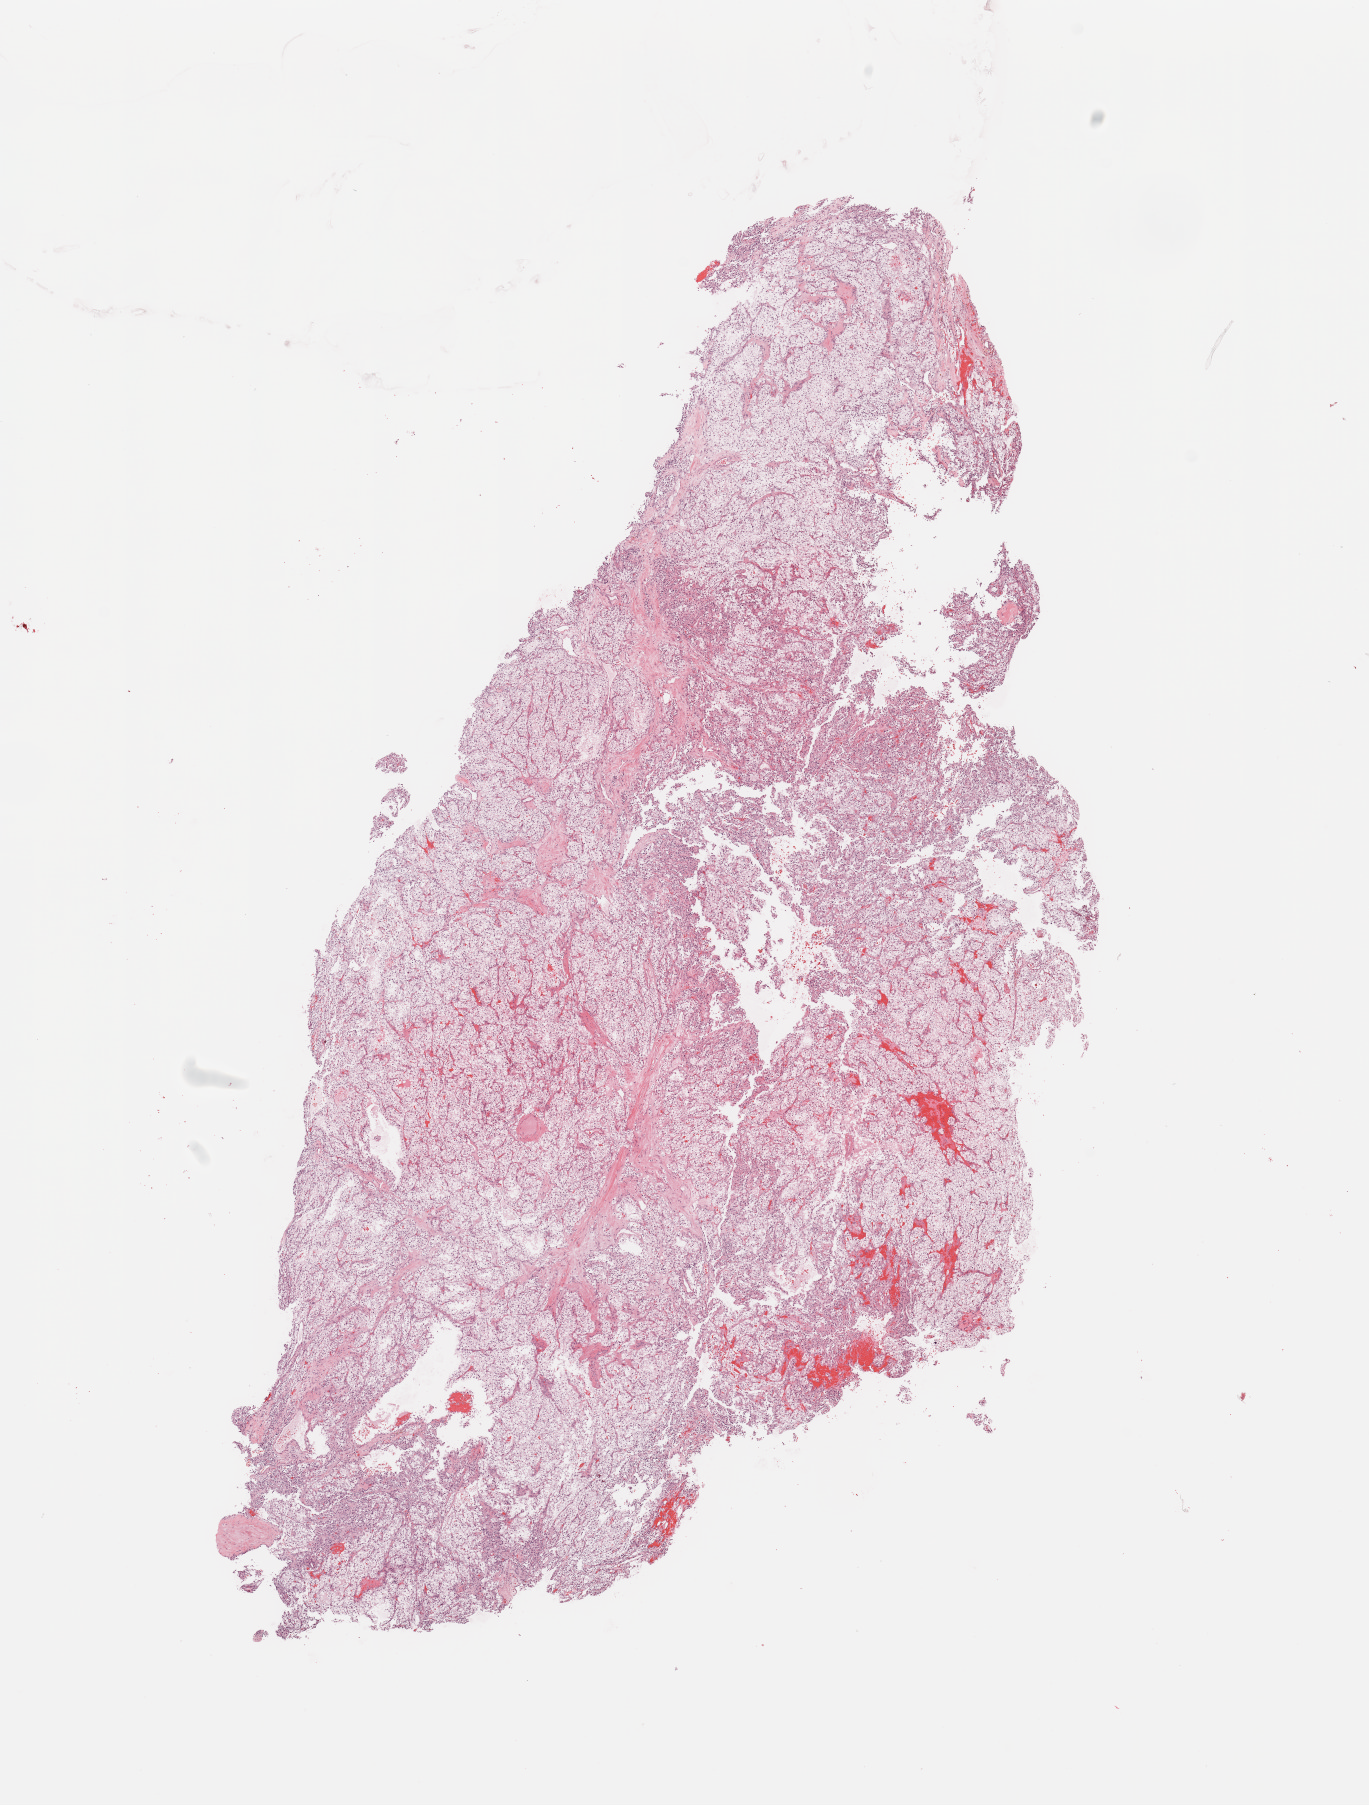
Whole-slide histology image, H&E-stained — whole scanned area (about 10.8 x 14.3 mm, acquisition: 20x scan) shown as a low-resolution overview. Tumour tissue sample, sampled site: kidney. 41-year-old male patient.
Diagnosis: Renal cell carcinoma, NOS.